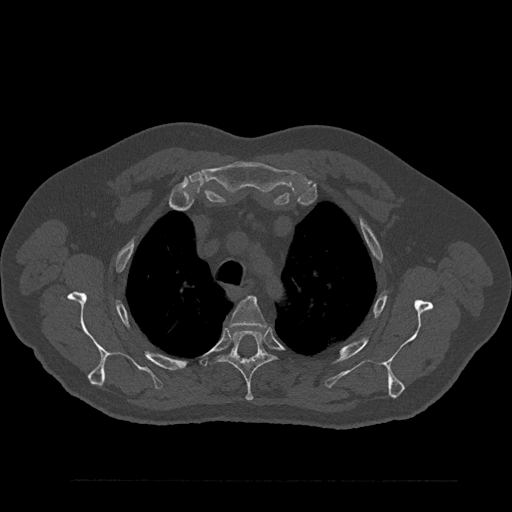
CT including the spine, one axial slice; slice 652 of 797 in the series (ordered by position); reconstruction kernel Br40s/3; 120 kVp; bone window (W 1800 / L 400 HU); 0.5 mm slice thickness; 512 × 512 image matrix, field of view 430 × 430 mm. Male patient, age 61 years. Case-level facts recorded for this patient, not image findings: primary cancer: prostate.
Structures marked on this image (semi-automatic segmentation, software-assisted and operator-edited):
- T3 vertebra: bounding box <230,297,266,328> (left, top, right, bottom; pixels)
- T4 vertebra: <218,329,274,401>